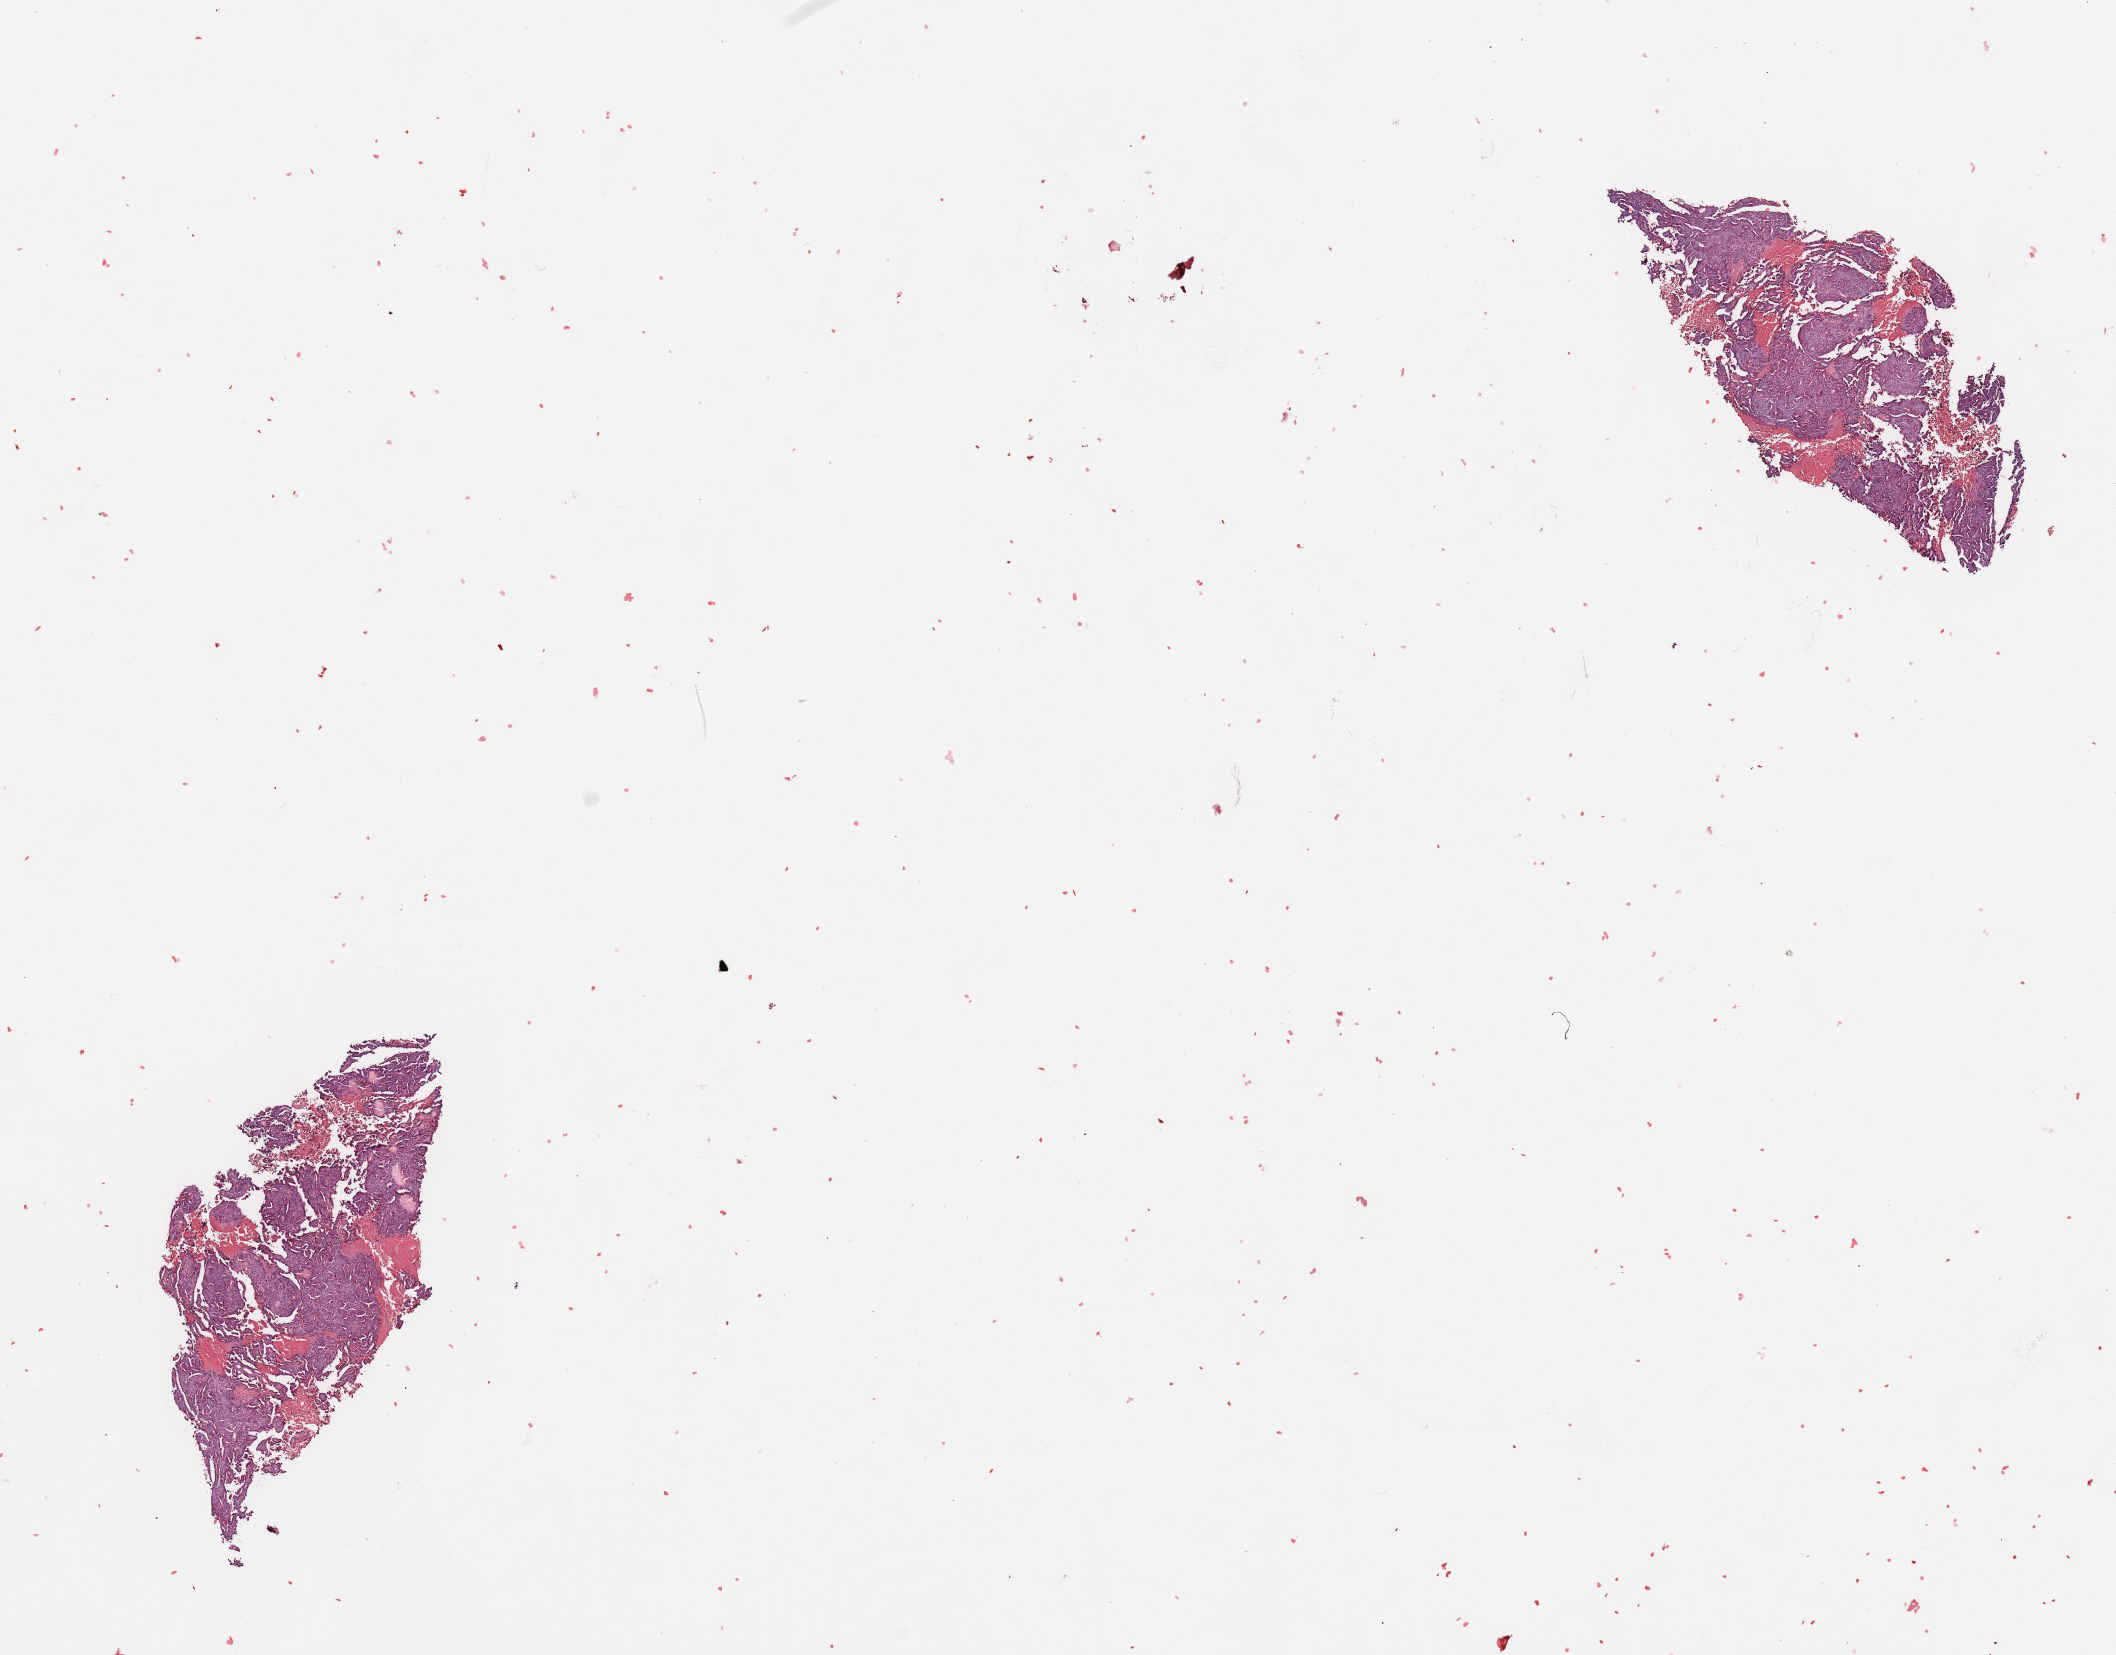
Digitized H&E-stained tissue section (whole slide), shown as a low-resolution overview of the whole scanned area (about 16.7 x 13.1 mm, from a 20x scan), uterus, tumour tissue. 73-year-old female patient. Histologic grade: G3 (poorly differentiated).
Diagnosis: Endometrioid adenocarcinoma, NOS. AJCC pathologic stage: II.